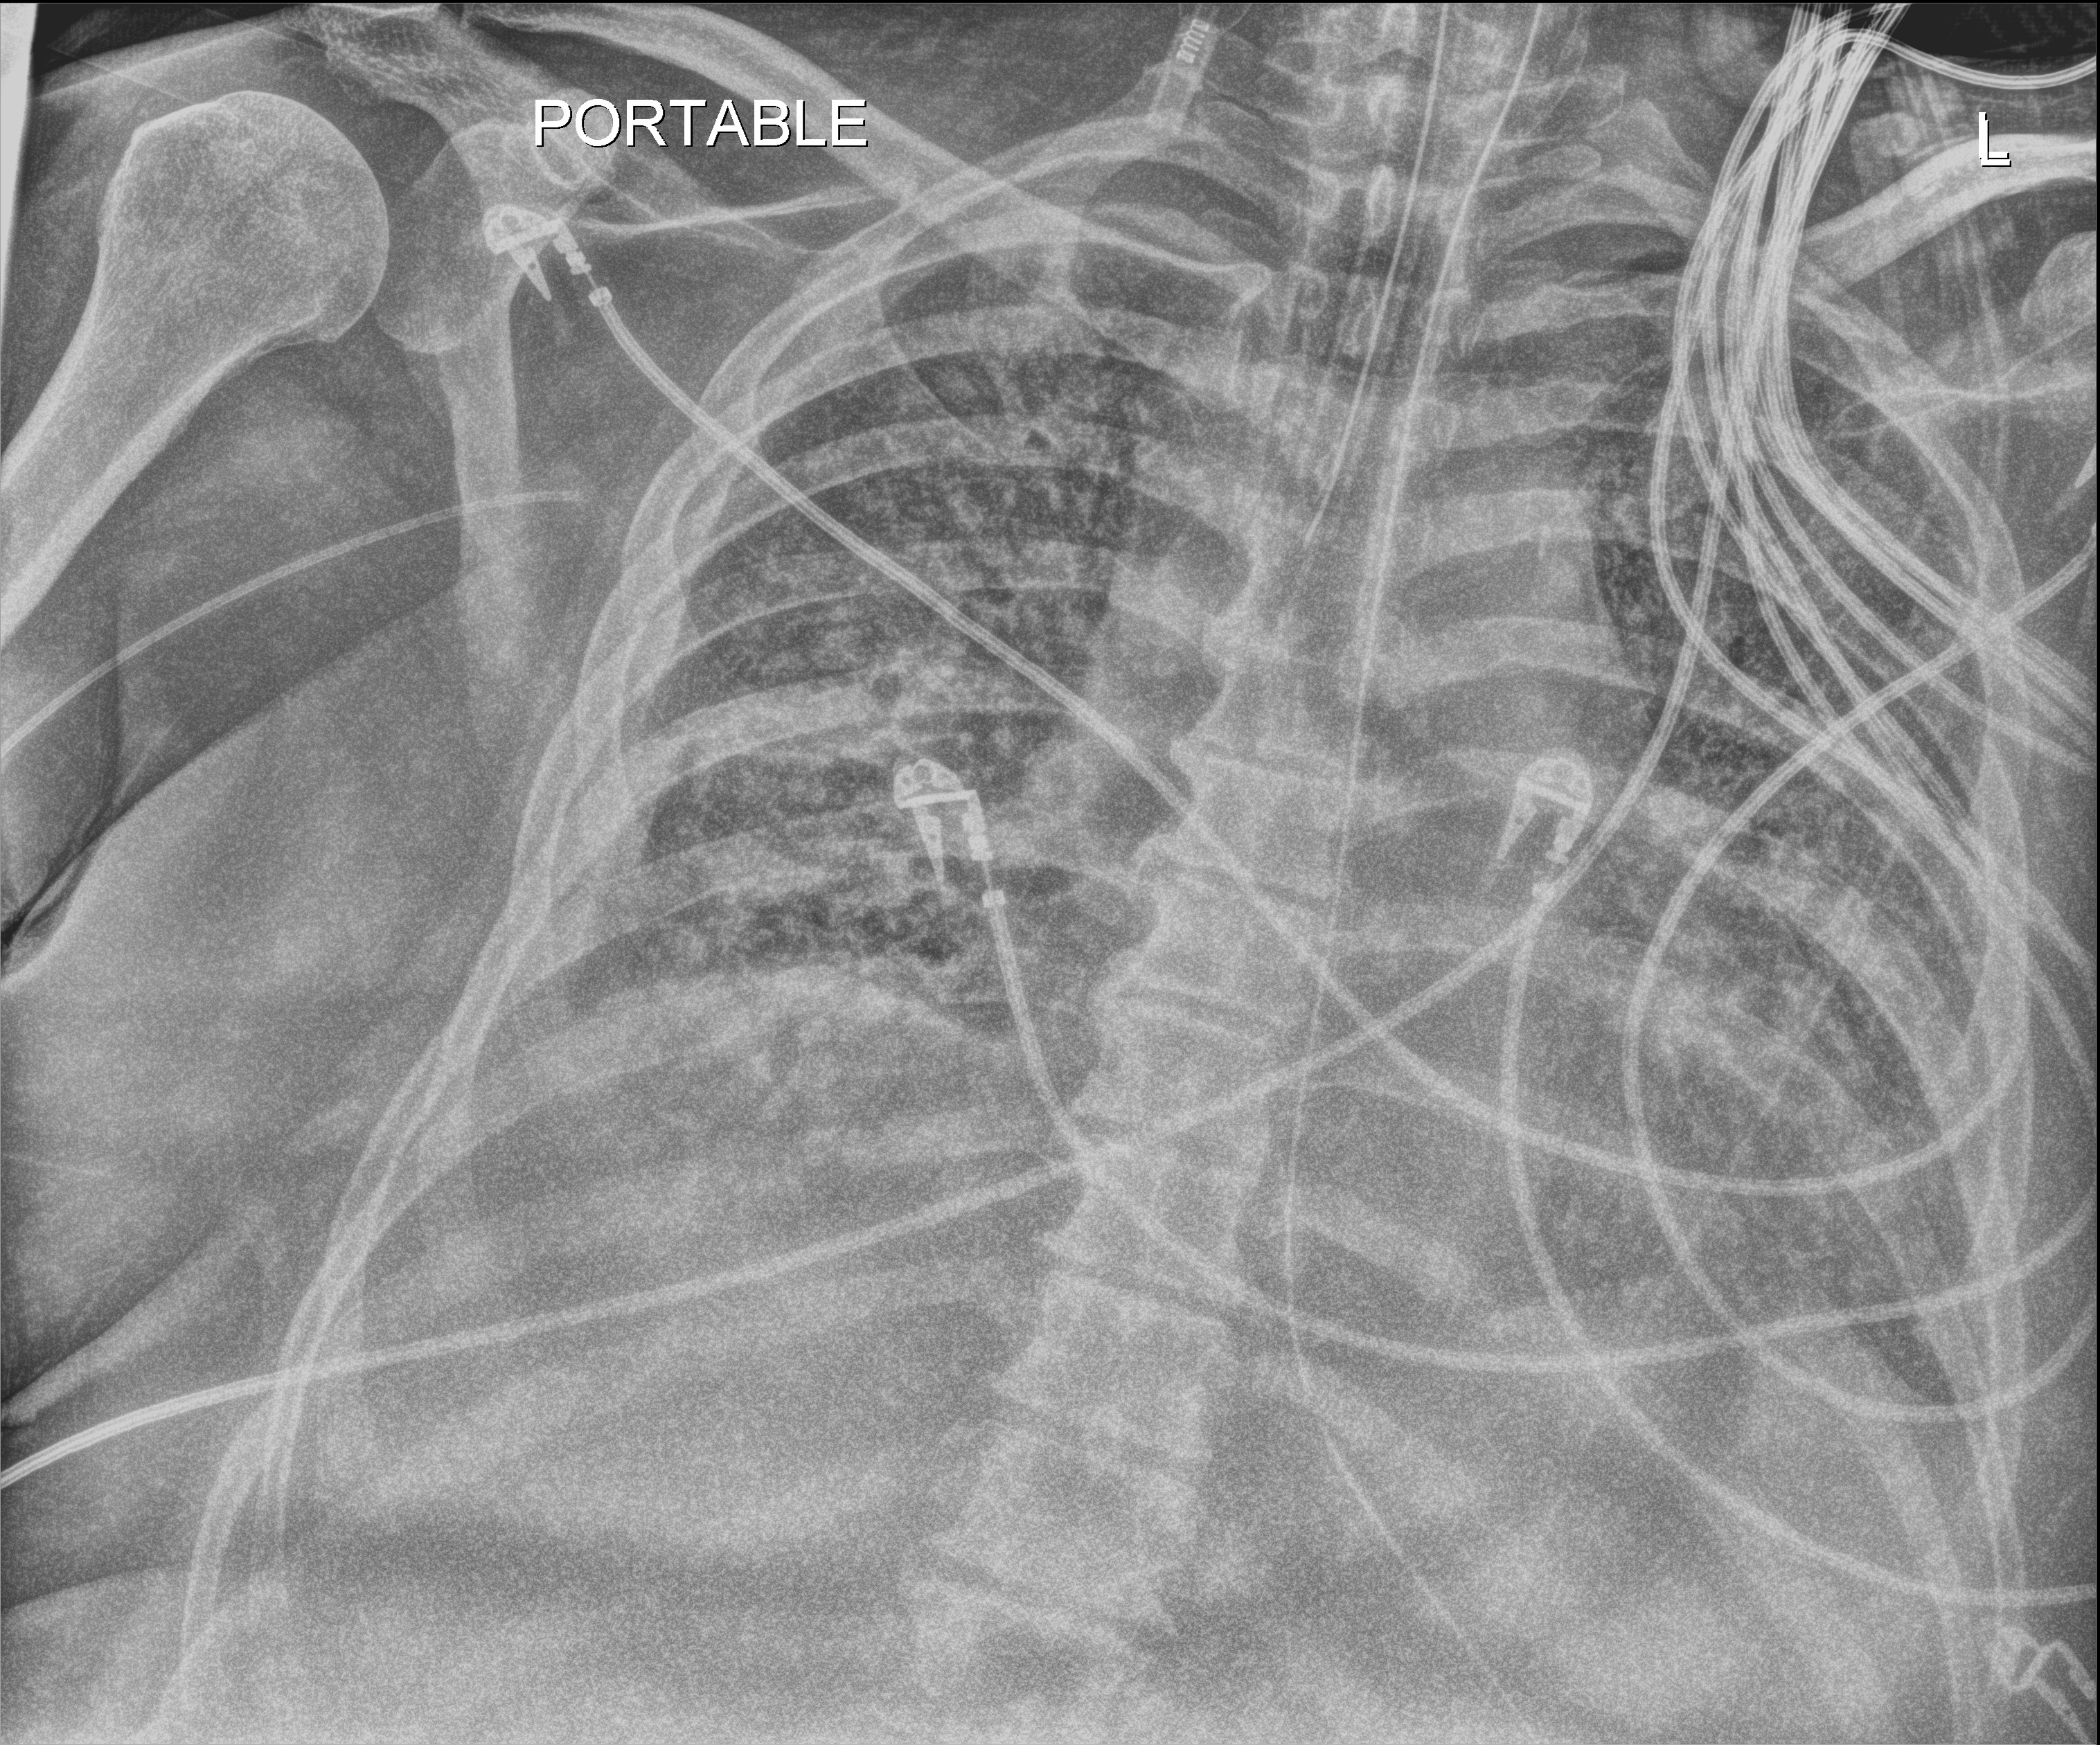
Portable chest radiograph; anteroposterior (AP) projection. Patient hospitalised with COVID-19; male, aged 60–74 years.
Hospital-stay facts (about this admission, not read from this image; timing relative to this image not recorded):
- admitted to intensive care during this hospital stay: yes